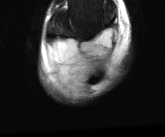
MRI of an extremity soft-tissue mass, one axial slice. Position 12 of 81 along the scan axis. T2-weighted fat-saturated. MR volume resampled by the dataset authors to the PET/CT grid (not the native acquisition matrix). 165 × 137 image matrix, field of view 161 × 134 mm. Male patient. Case-level facts recorded for this patient, not image findings: histological type: liposarcoma - round cell; grade: high; site of the primary tumour: right calf.
Outlined on this slice (expert contour drawn on MRI and transferred to this co-registered scan by the dataset authors):
- gross tumour volume (mass): bounding box (x1, y1, x2, y2) in pixels: (46, 39, 118, 97)